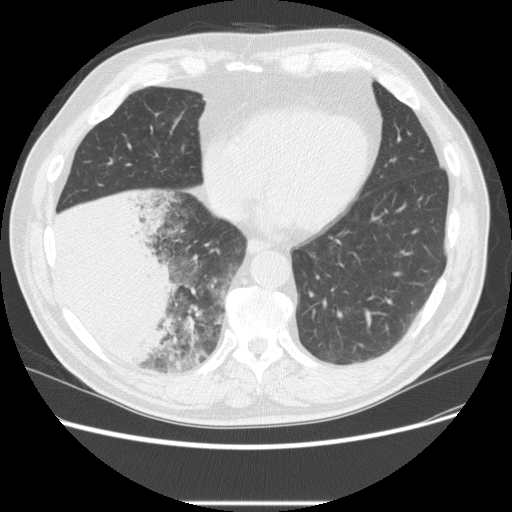
Low-dose screening chest CT, one axial slice. Position 72 of 233 along the scan axis. 120 kVp. Lung window (W 1500 / L -600 HU). 512 × 512 image matrix.
Outlined on this slice (expert manual segmentation):
- lesion 3 (tumor, lower lobe of right lung): bounding box [x1, y1, x2, y2] px = [52, 190, 178, 368]